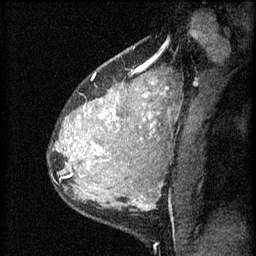
Breast MRI (dynamic contrast-enhanced), one sagittal slice; position 44 of 60 along the scan axis; 3 images stored at this slice position (order not interpretable as contrast timing); 1.5 T; TE 4.2 ms, TR 8.2 ms; 2 mm slice thickness; 256 × 256 image matrix. Patient: female, 37 years.
Structures marked on this image (semi-automatic segmentation, software-assisted and operator-edited):
- analysis volume of interest (the breast-tissue region the enhancement analysis was run in; not a lesion): bounding box (x1, y1, x2, y2) in pixels: (53, 78, 140, 181)
- tumour enhancement mask (voxels above the 70 % enhancement threshold inside the analysis volume of interest): (71, 106, 118, 175)